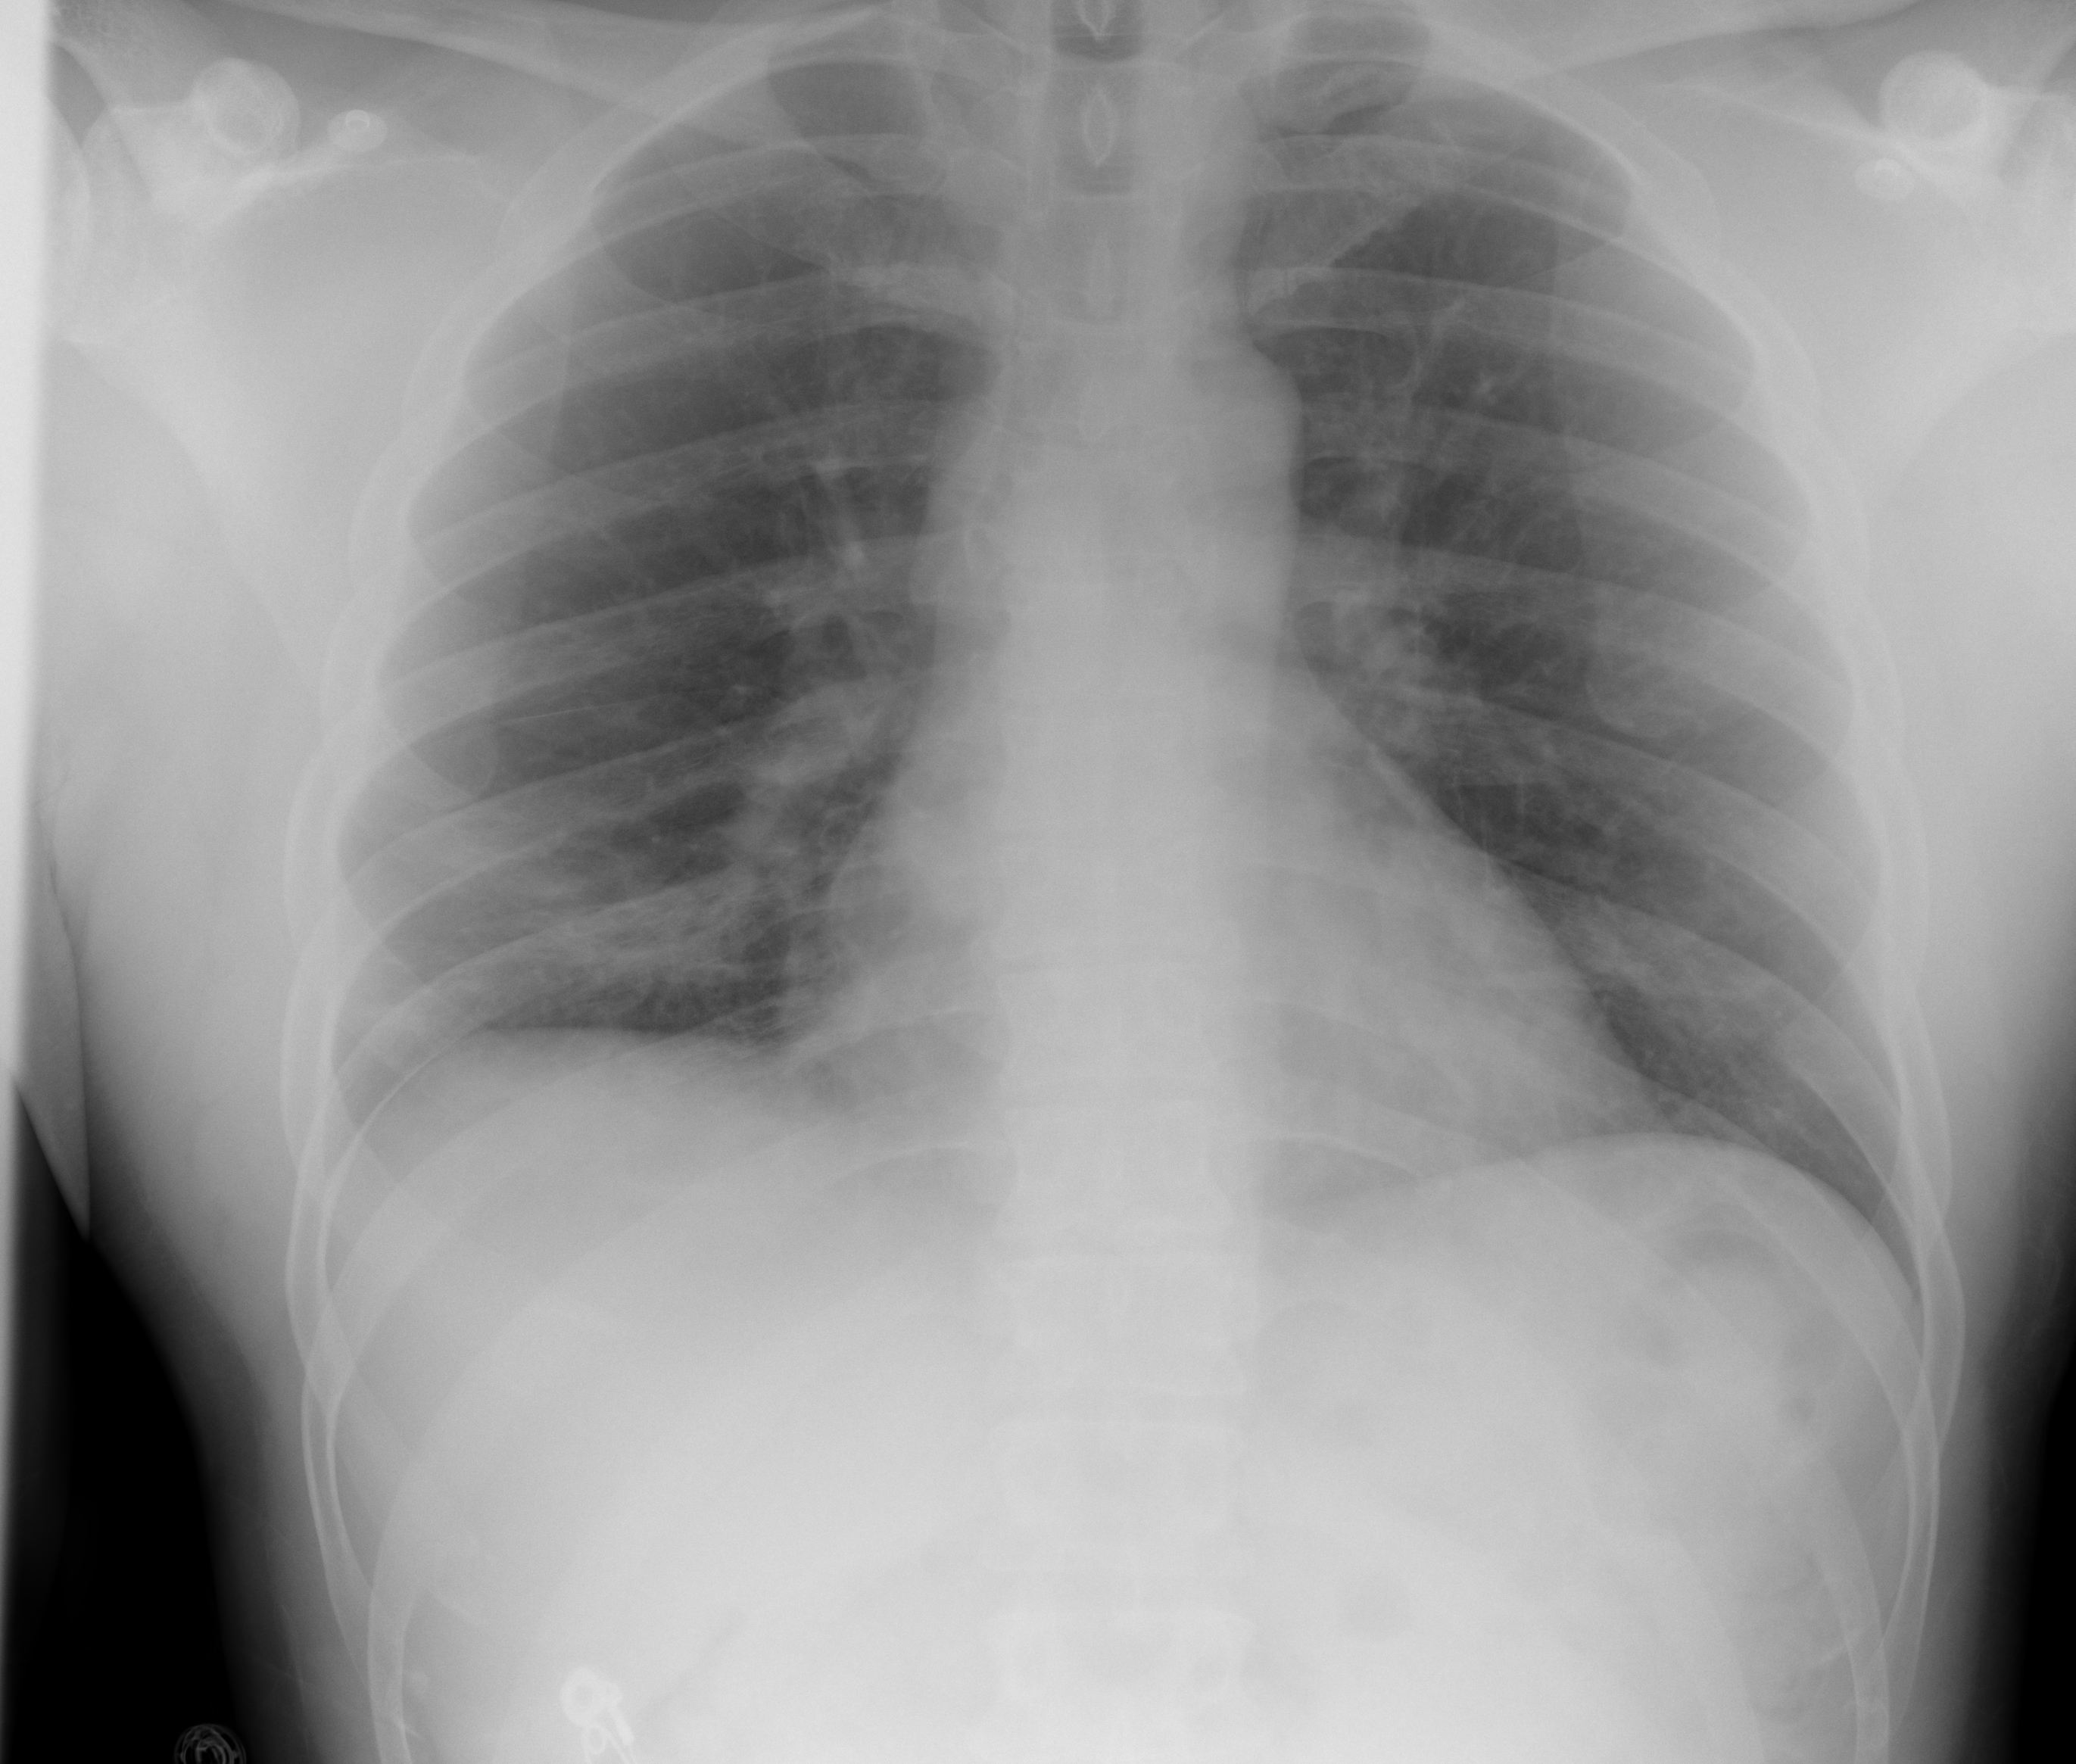
Chest X-ray (portable), AP projection. Male patient, age 44 years; imaged 6 days after the COVID-19 diagnosis.
Radiologist's key findings for this exam: hazy opacities within the right lung base and to a lesser extent within the left lung base.